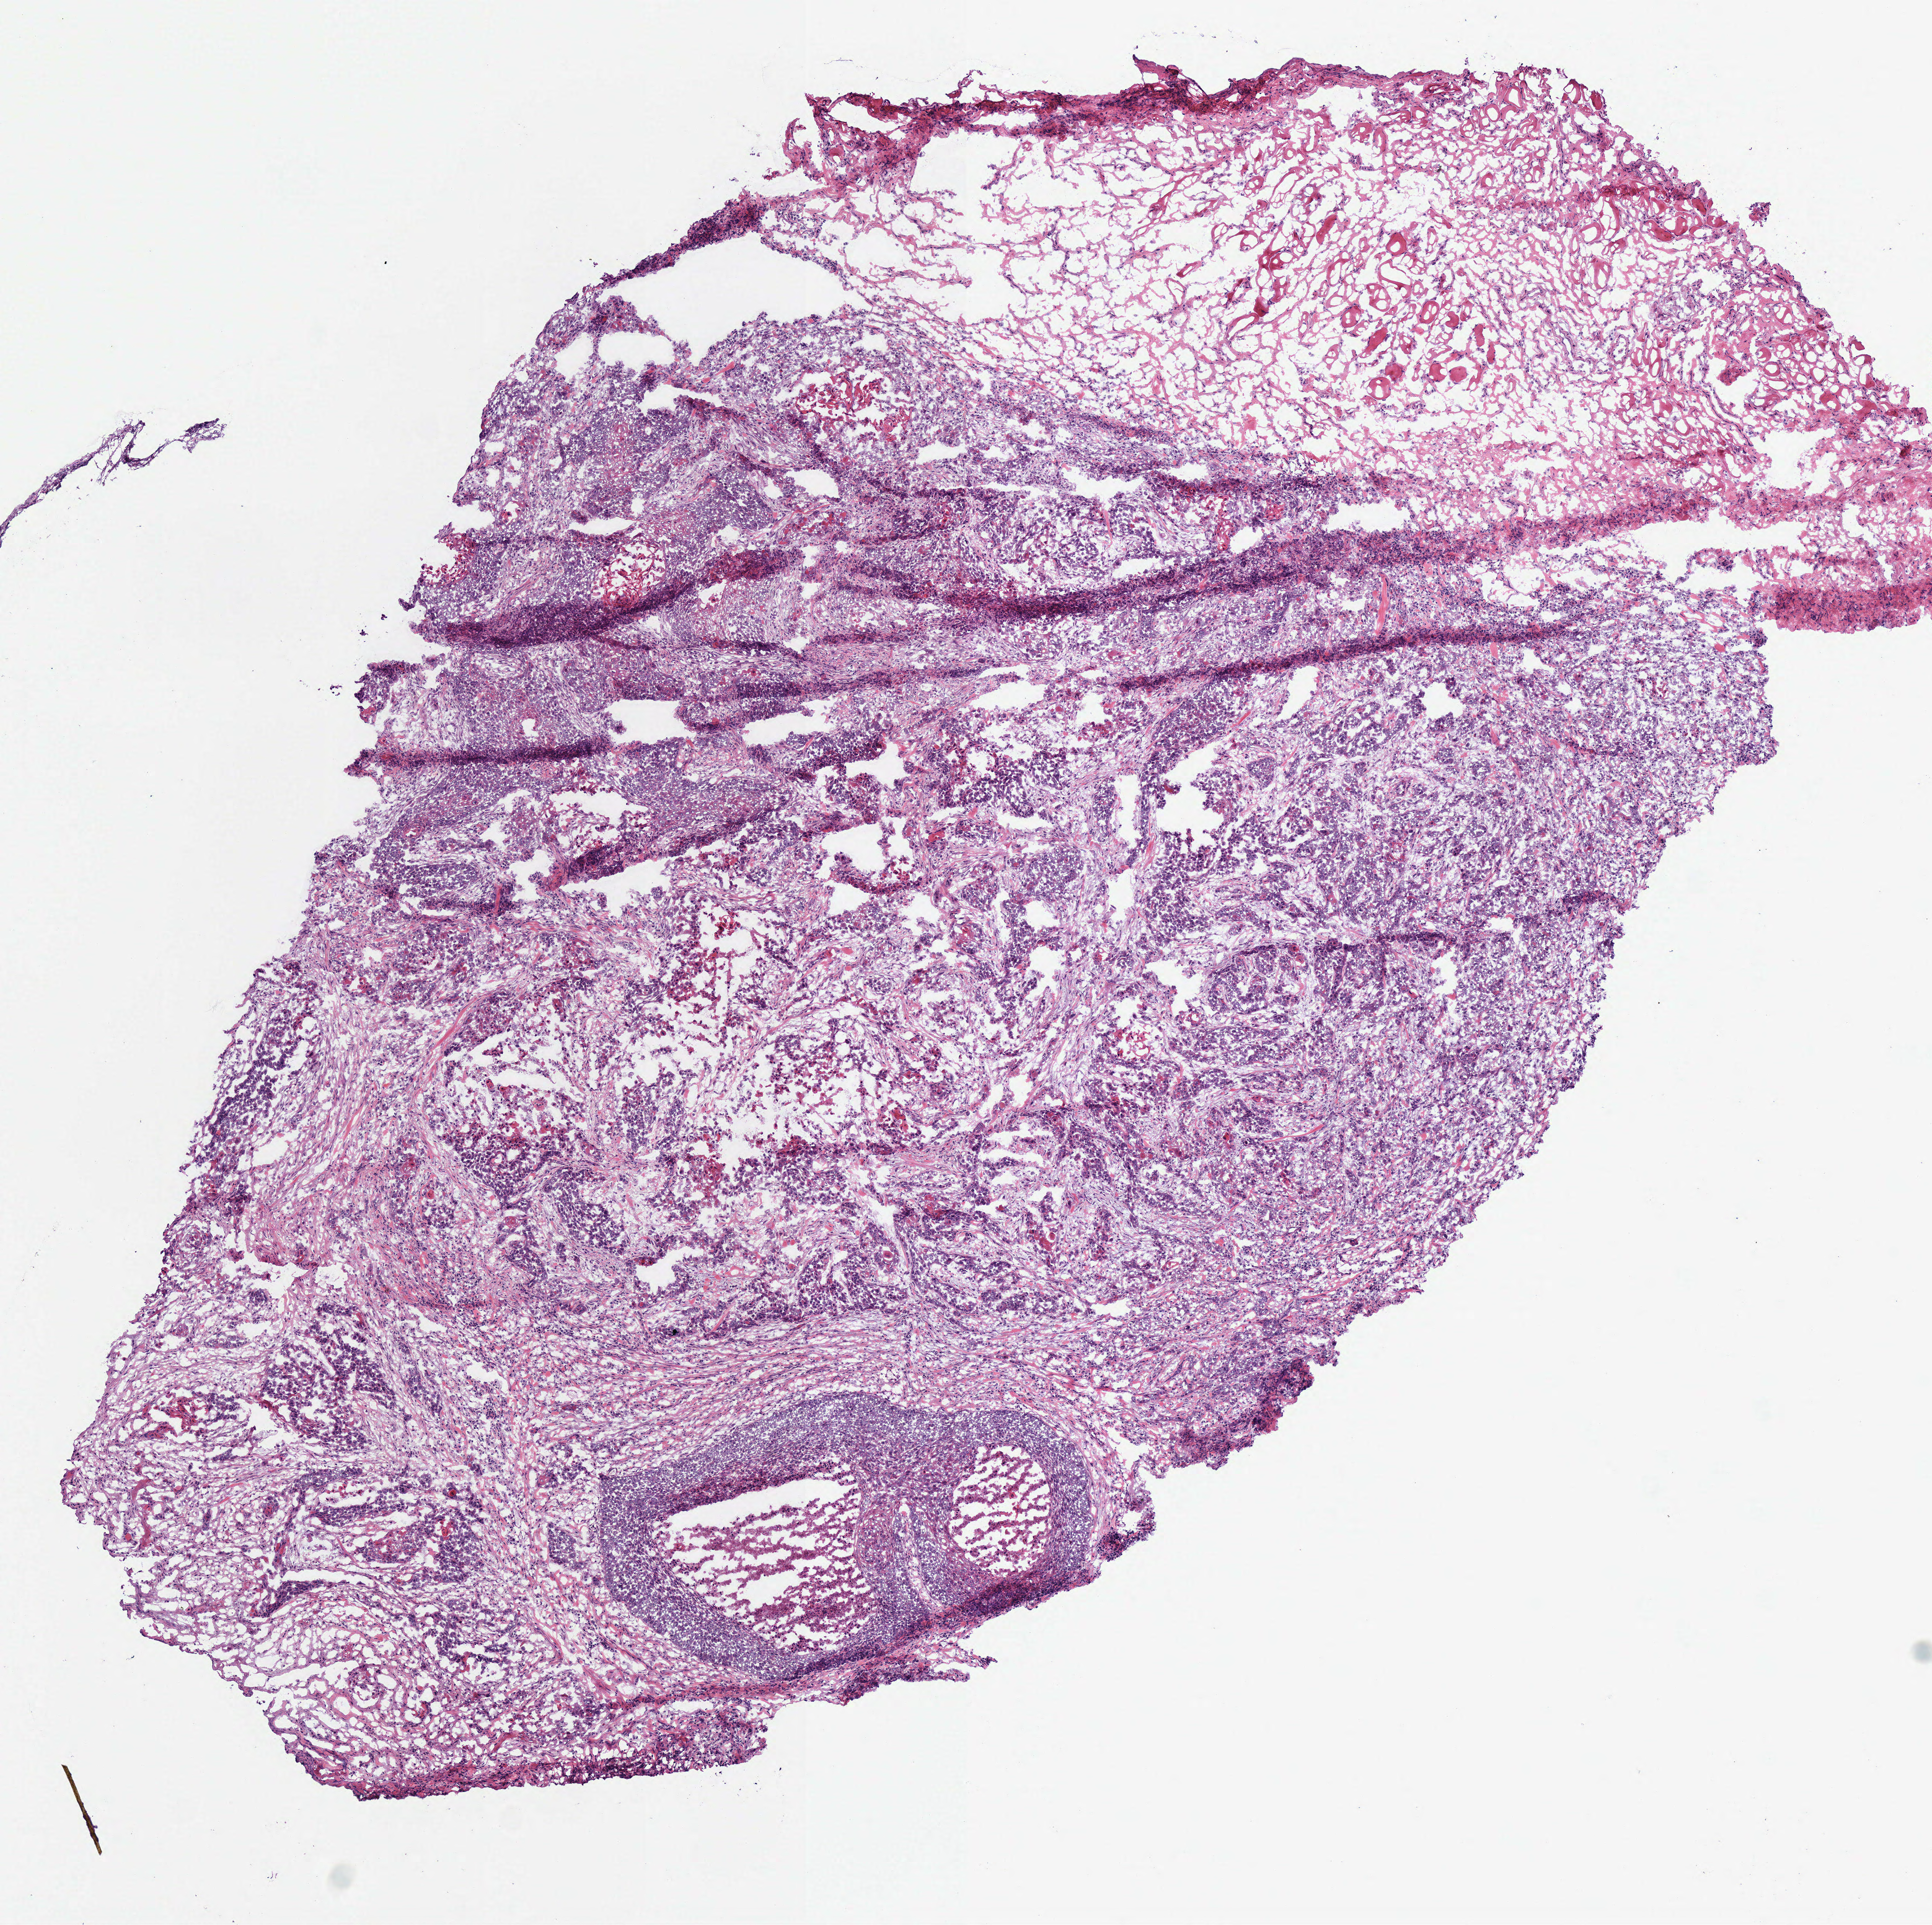
Whole-slide histology image, H&E — whole scanned area (about 5.9 x 5.9 mm, acquisition: 40x scan) shown as a low-resolution overview, frozen section from the bottom of the tissue portion, primary tumour sample from the head and neck. Male, age 64 years at initial diagnosis.
Histologic diagnosis: Squamous cell carcinoma, NOS (larynx, NOS).